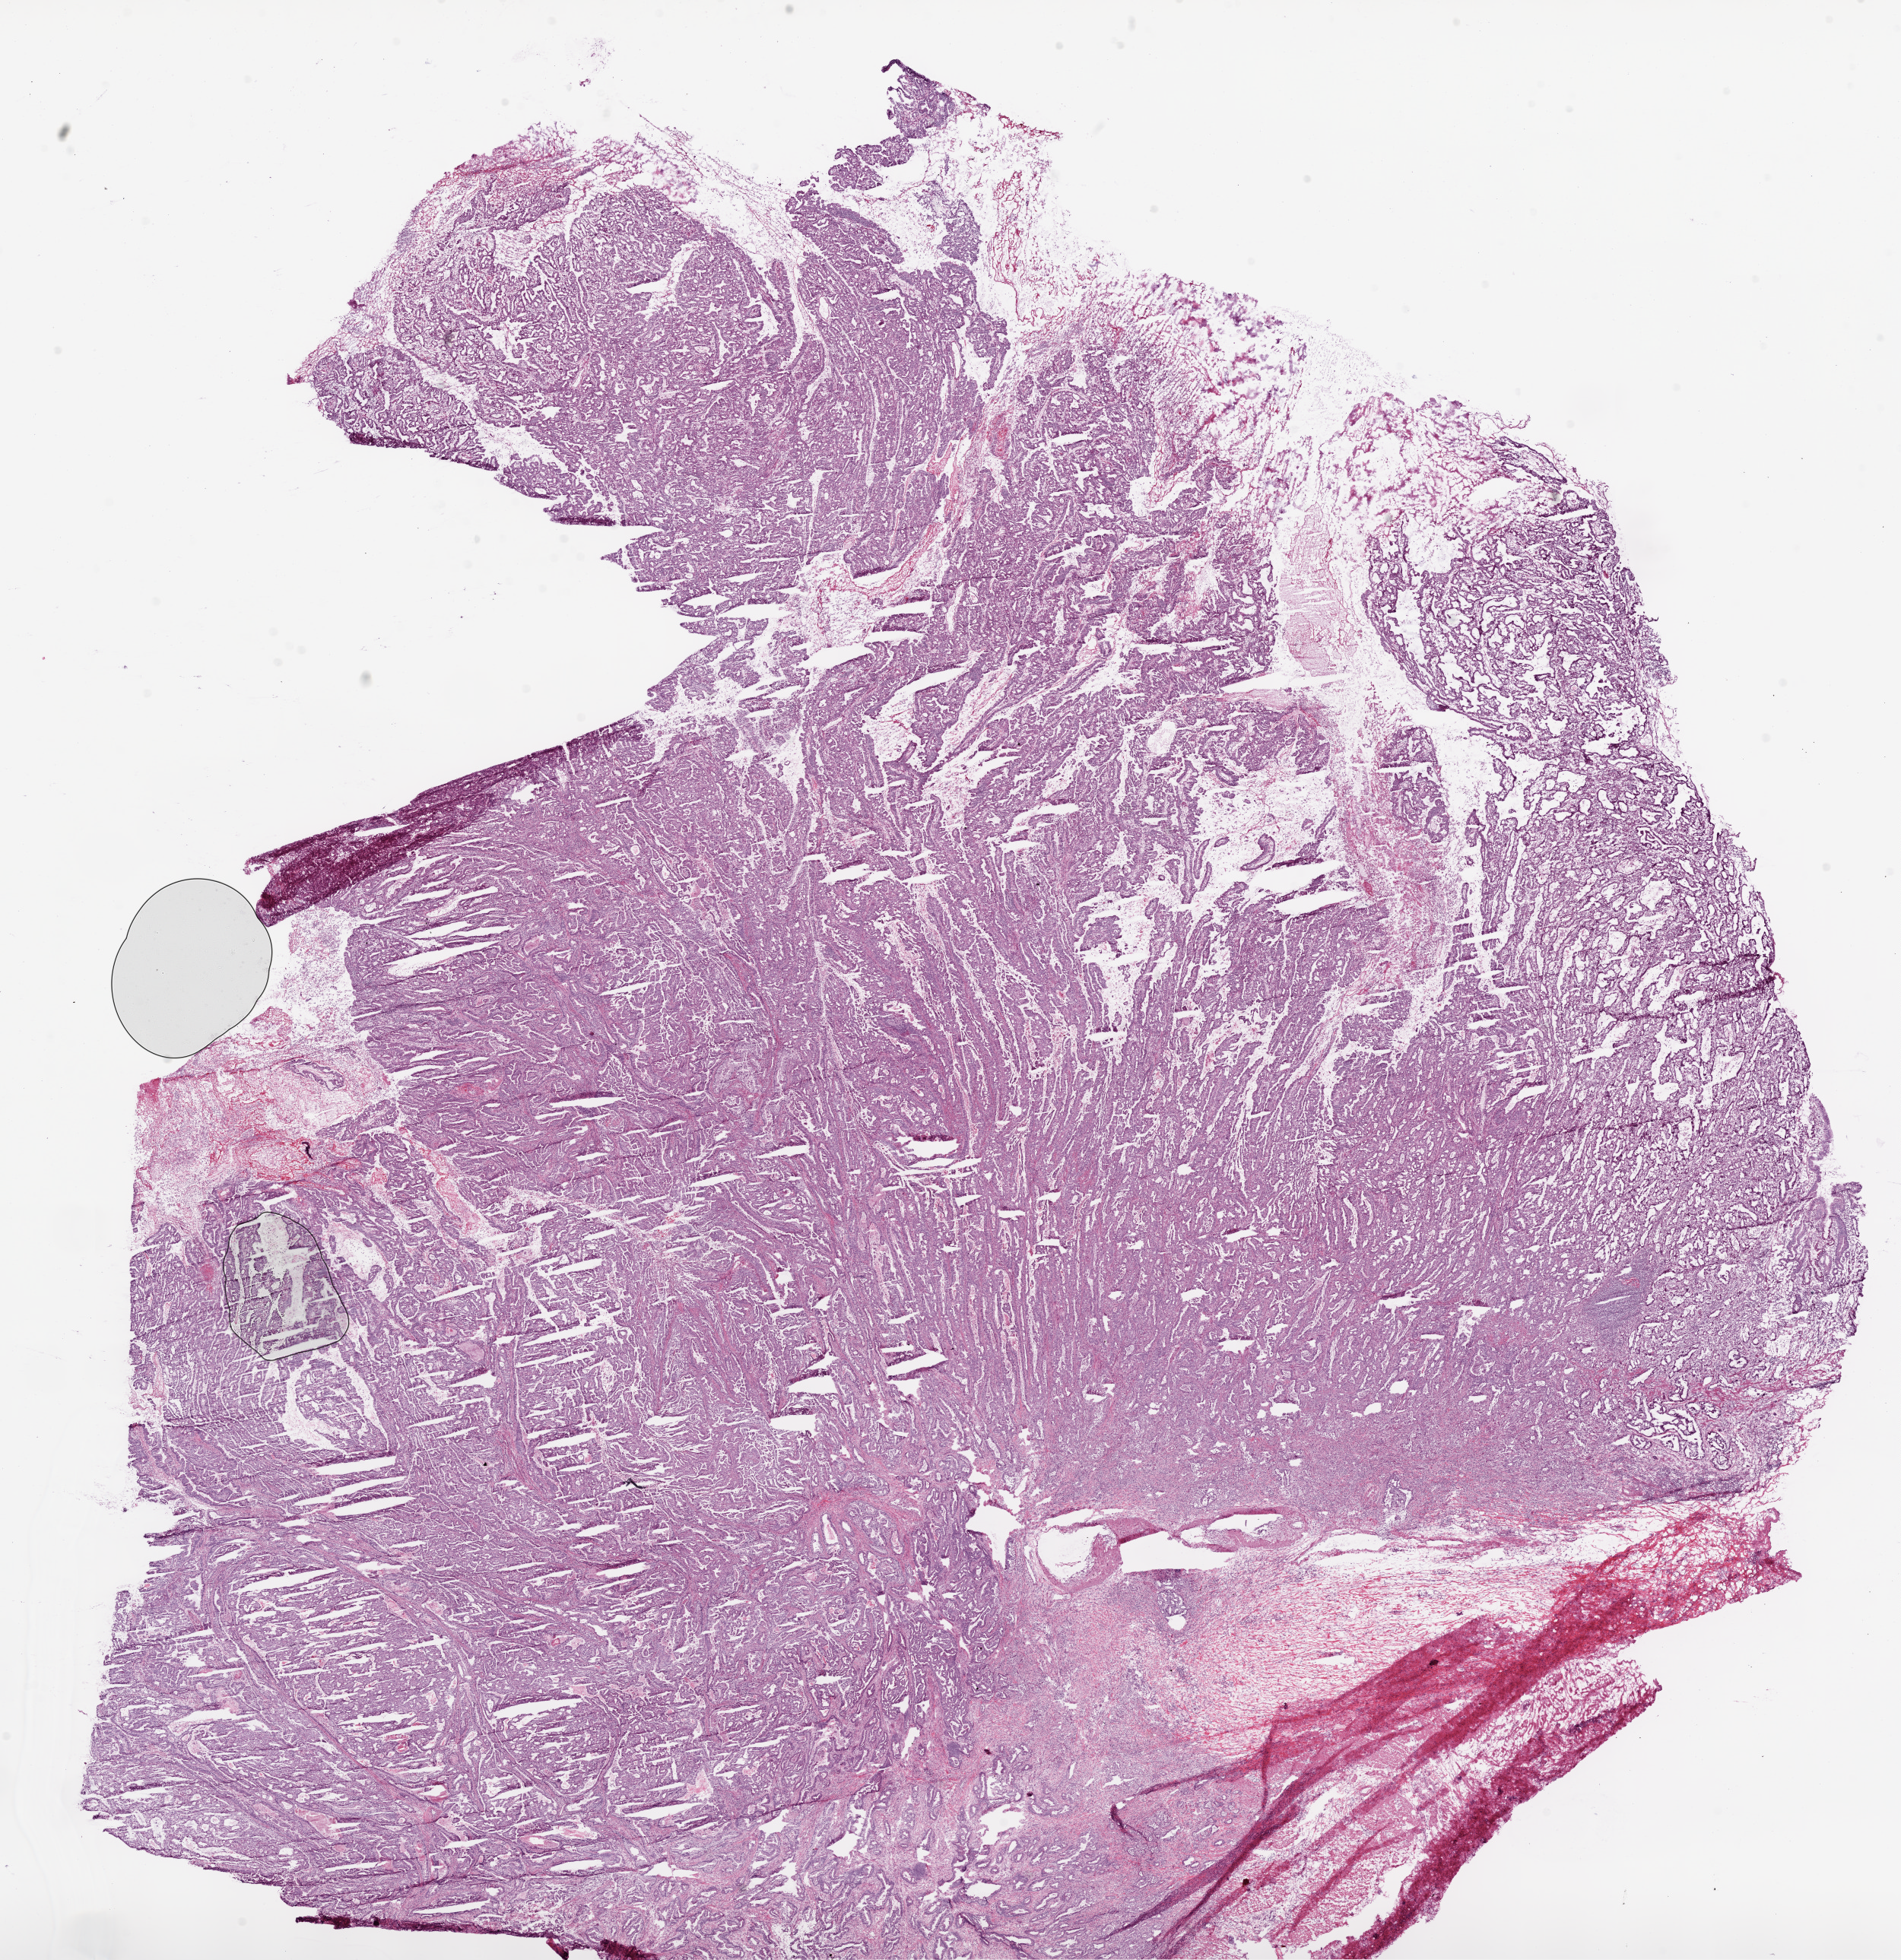
Hematoxylin and eosin (H&E) stained whole-slide image, shown as a low-resolution overview of the whole scanned area (about 20.1 x 20.7 mm, from a 20x scan); frozen section from the bottom of the tissue portion; sample: primary tumour, stomach. Male, age 51 years at initial diagnosis. Histologic grade: G2 (moderately differentiated). Pathologist review of this section (percent, as recorded): tumour cells 95%, tumour nuclei 85%, normal cells 0%, stromal cells 3%, necrosis 2%.
AJCC pathologic stage: IB. Lymph nodes positive (case pathology): 0 of 6 examined. Diagnosis: Adenocarcinoma, NOS (body of stomach).